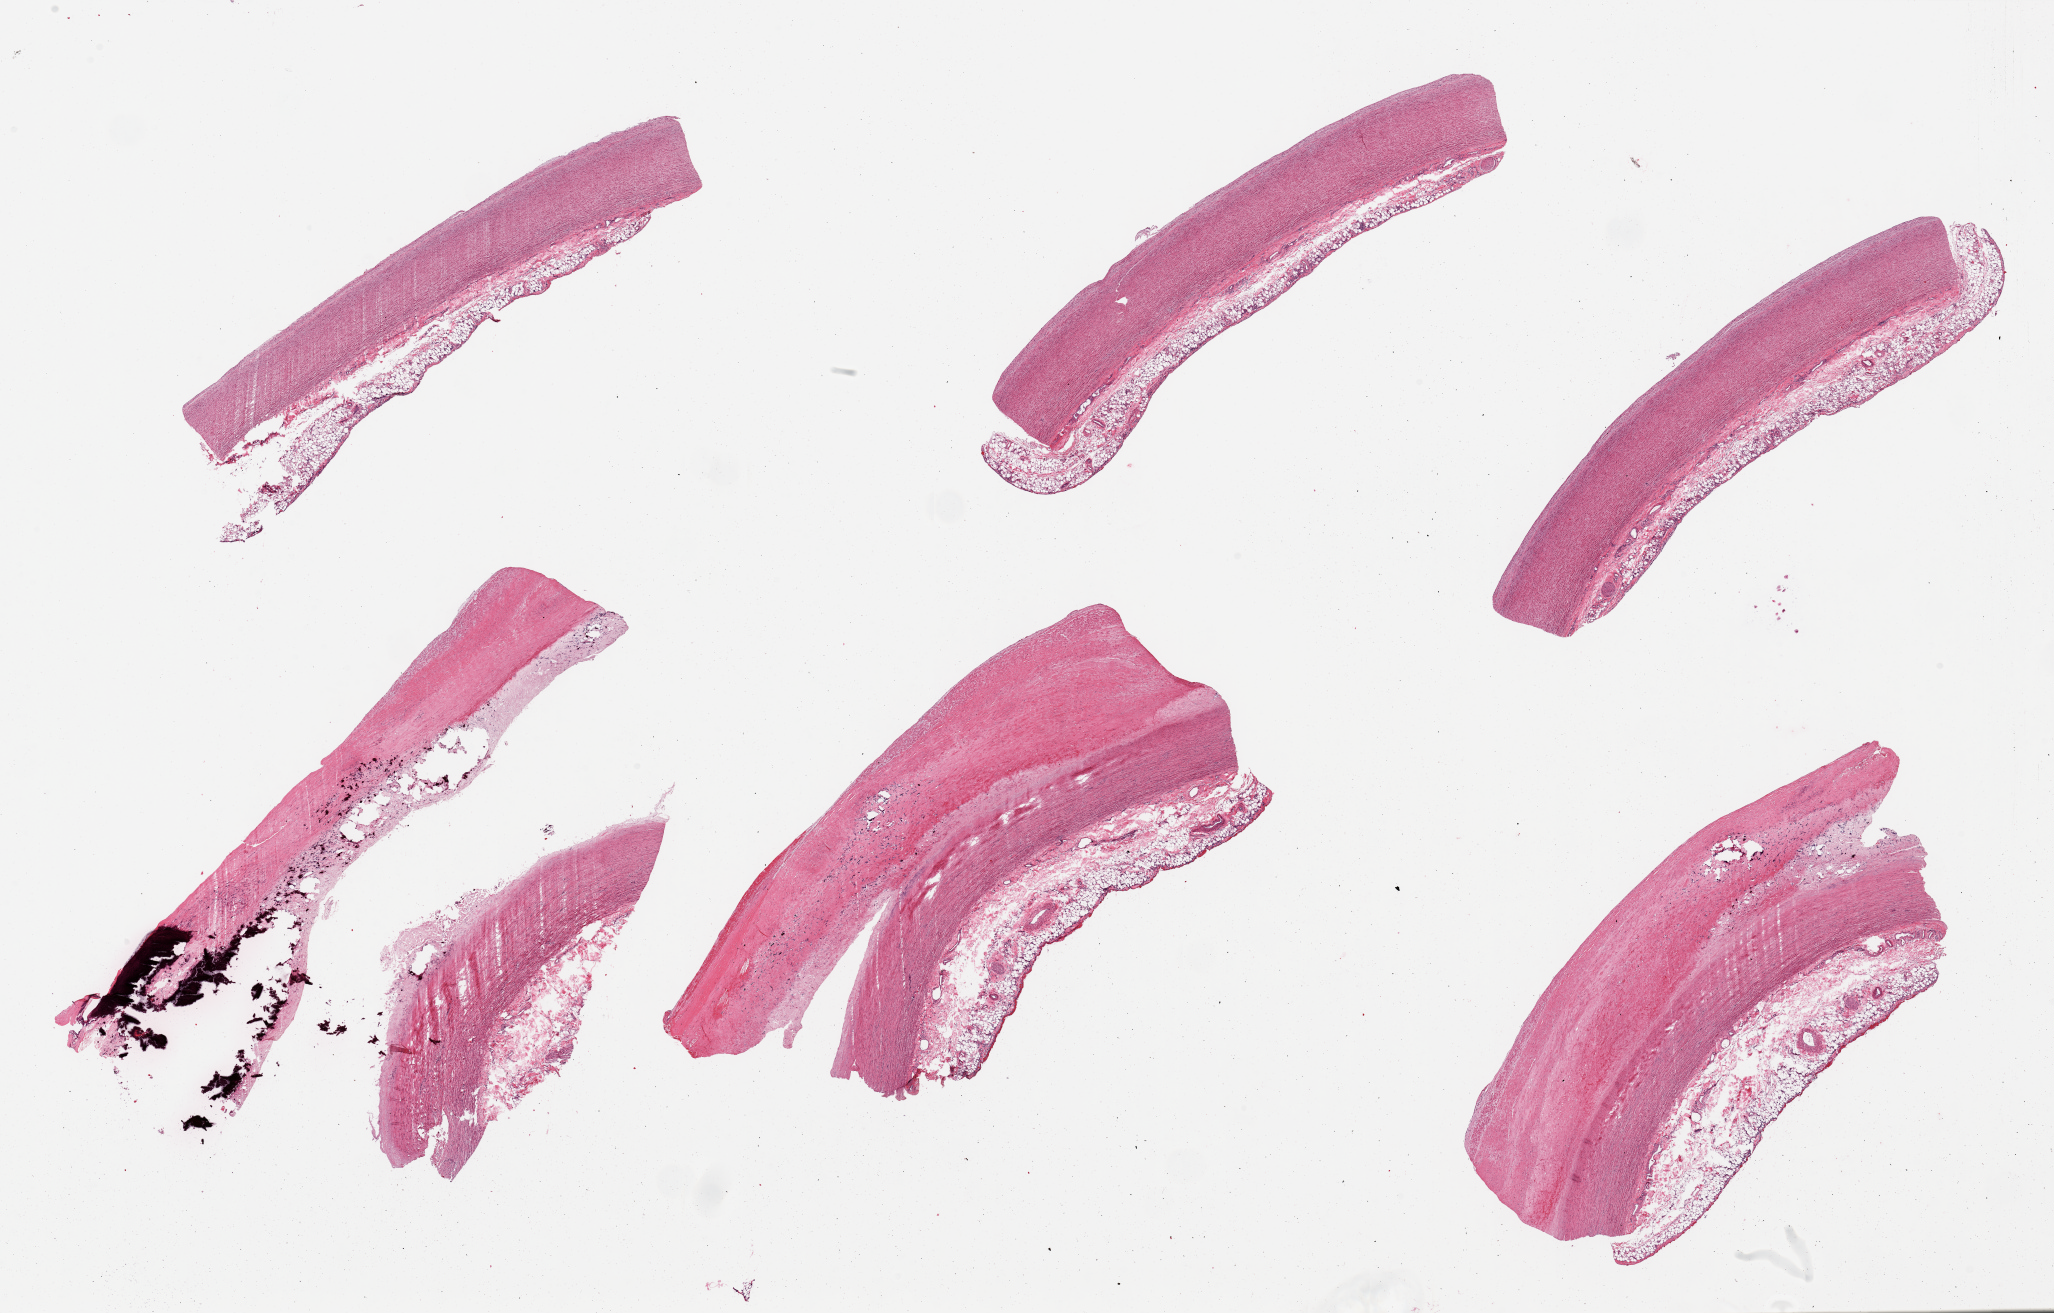
Digitized H&E-stained section, brightfield, a low-resolution overview of the entire scanned area, about 32.5 x 20.8 mm (from a 20x scan), PAXgene-fixed, paraffin-embedded tissue, target tissue: aorta, donor tissue sample. Donor sex: male.
Pathologist's review note for this sample: 6 pieces; large calcified plaques.